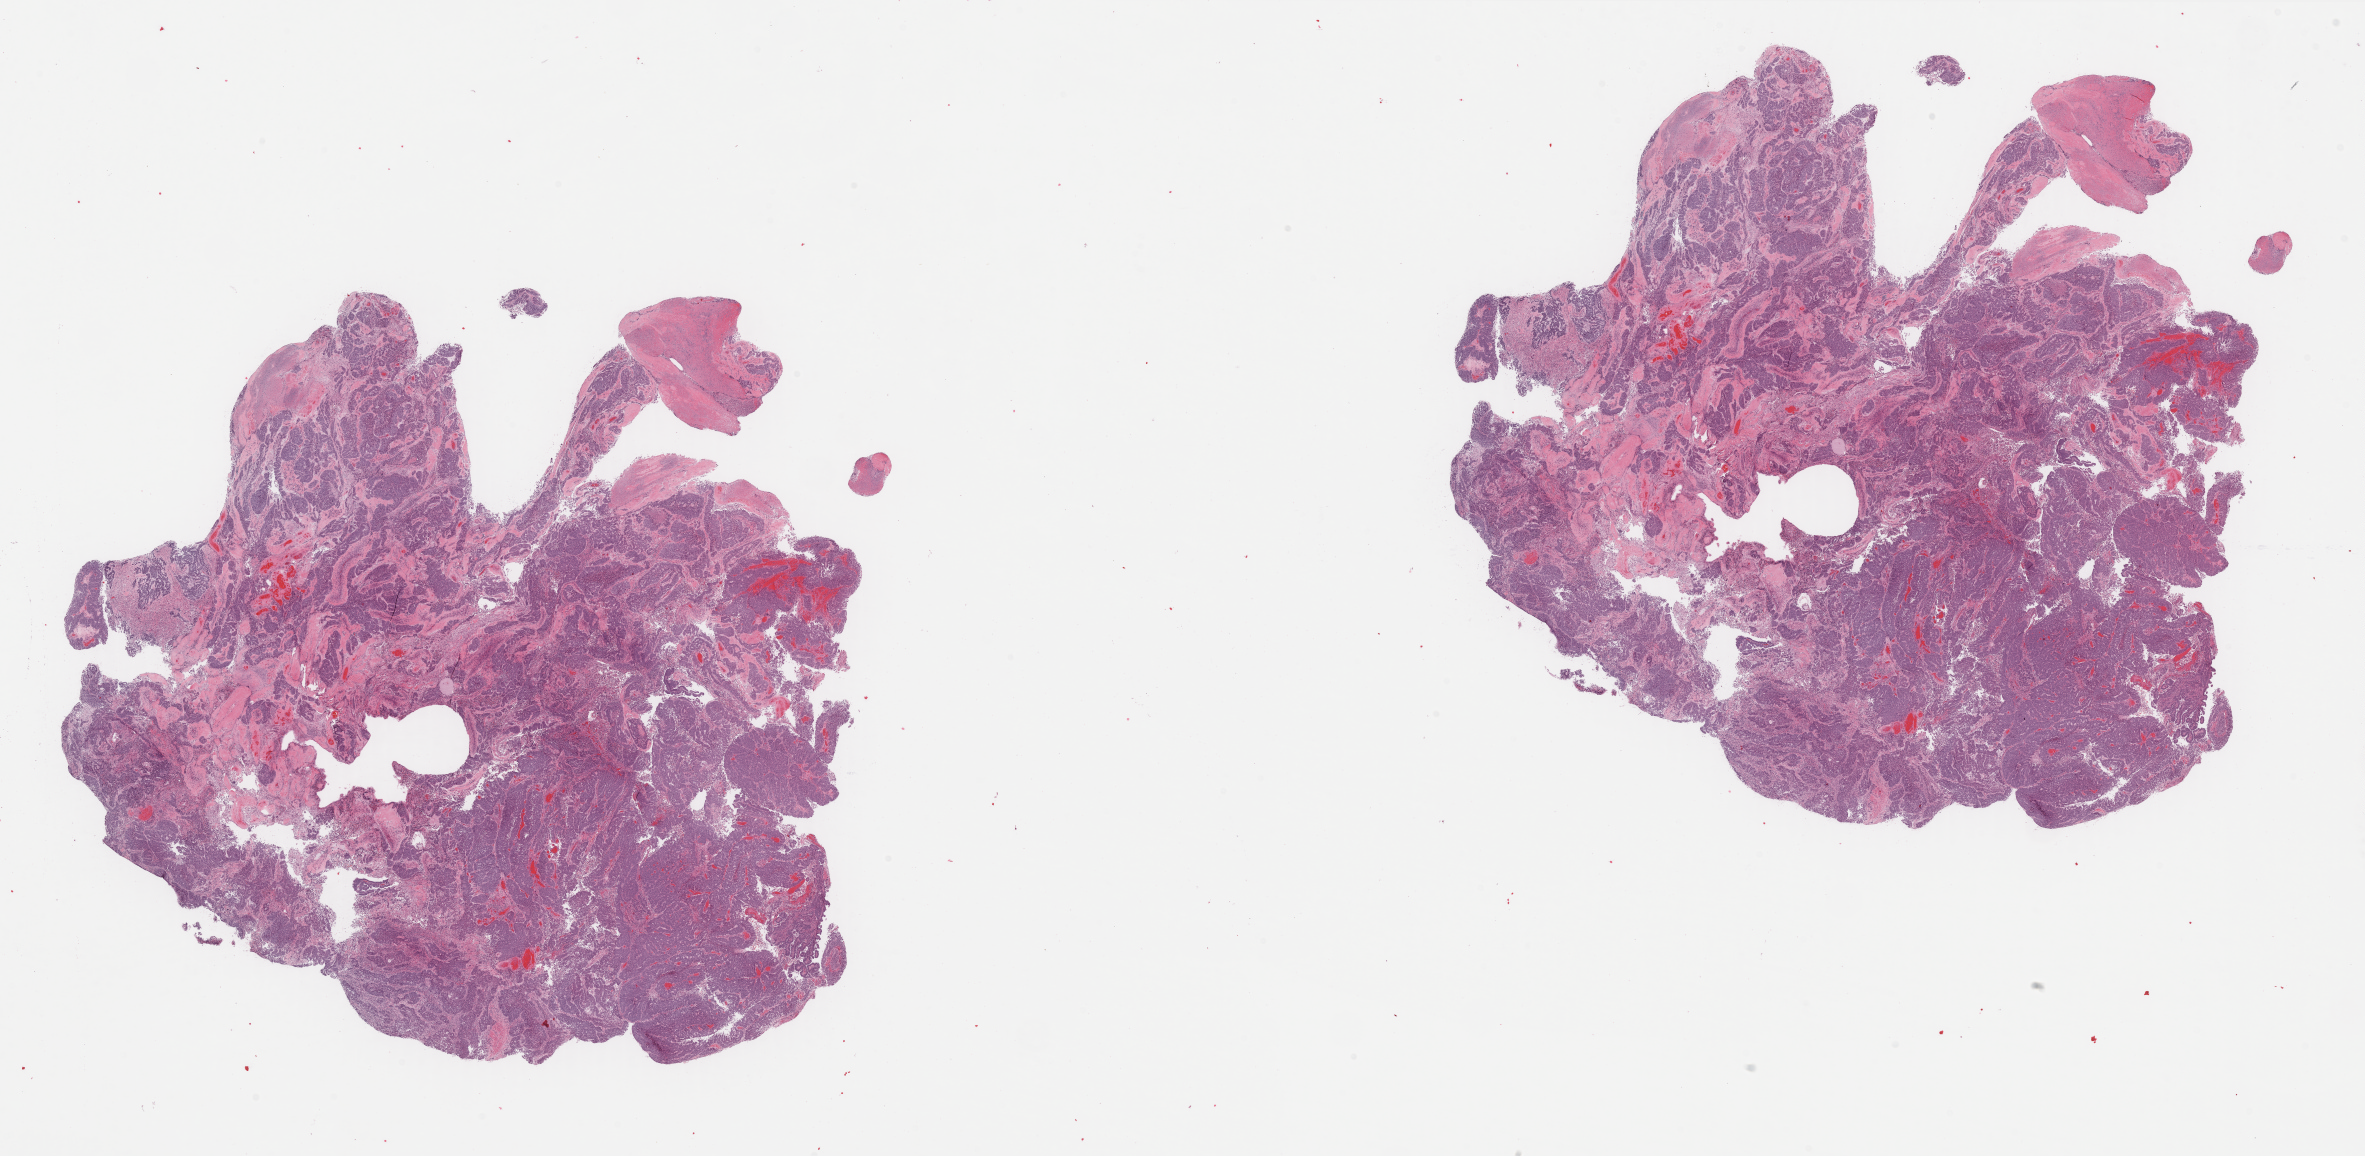
Whole-slide histology image, H&E-stained, low-resolution overview of the scanned area, about 37.4 x 18.3 mm (from a 40x scan). FFPE section. Uterus, primary tumour sample. Female, age 64 years at initial diagnosis. Histologic grade: G3 (poorly differentiated).
Diagnosis: Serous cystadenocarcinoma, NOS (endometrium). FIGO stage: IVB.